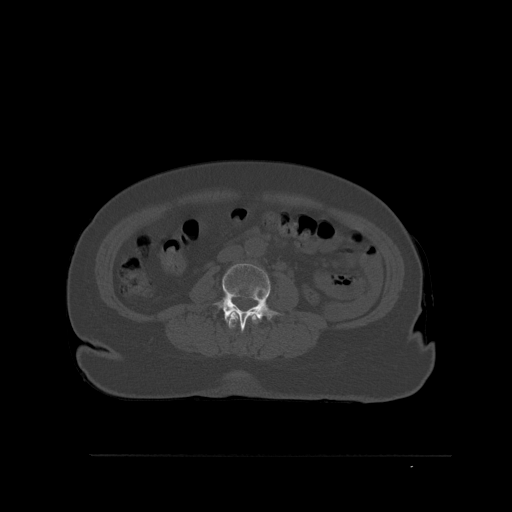
CT including the spine, one axial slice. Position 226 of 527 along the scan axis. Bone window (W 1800 / L 400 HU). 512 × 512 image matrix. Female patient, age 73 years. Case-level facts recorded for this patient, not image findings: primary cancer: breast.
Outlined on this slice (semi-automatic segmentation, software-assisted and operator-edited):
- L2 vertebra: bounding box [x1, y1, x2, y2] px = [227, 312, 259, 329]
- L3 vertebra: [213, 263, 283, 332]